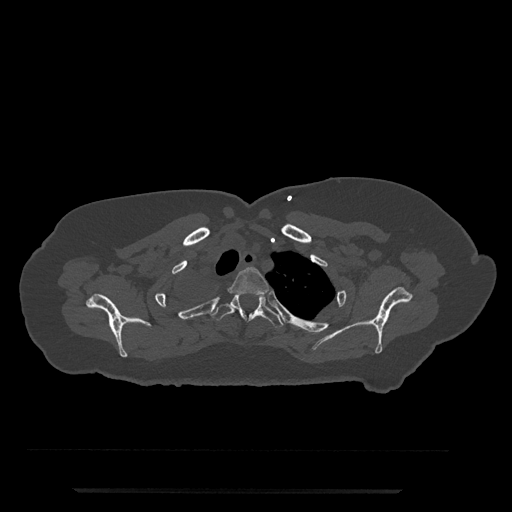
CT including the spine, one axial slice; position 649 of 797 along the scan axis; reconstruction kernel Br40s/3; 120 kVp; bone window (W 1800 / L 400 HU); 0.5 mm slice thickness; 512 × 512 image matrix. Patient: female, 51 years. Case-level facts recorded for this patient, not image findings: primary cancer: neuro.
Outlined on this slice (semi-automatically segmented with operator editing):
- T2 vertebra: bounding box [x1, y1, x2, y2] px = [229, 267, 269, 296]
- T3 vertebra: [195, 293, 284, 328]